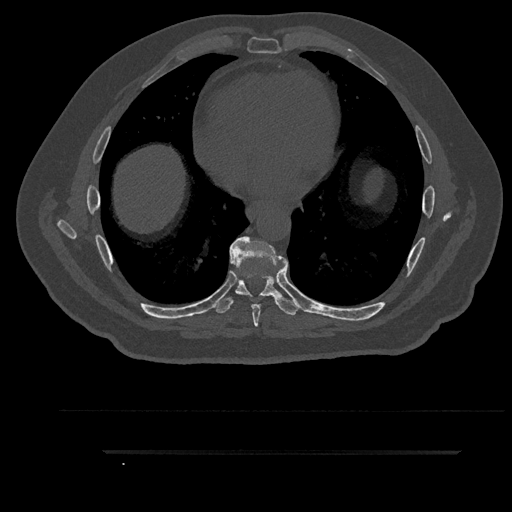
CT including the spine, one axial slice; position 500 of 797 along the scan axis; reconstruction kernel Br40s/3; 120 kVp; bone window (W 1800 / L 400 HU); 0.5 mm slice thickness; 512 × 512 image matrix, field of view 432 × 432 mm. Male patient, age 63 years. Case-level facts recorded for this patient, not image findings: primary cancer: renal.
Annotated regions visible in this slice (semi-automatic segmentation, software-assisted and operator-edited):
- T7 vertebra: bounding box (x1, y1, x2, y2) in pixels: (230, 236, 288, 327)
- T8 vertebra: (214, 248, 301, 315)